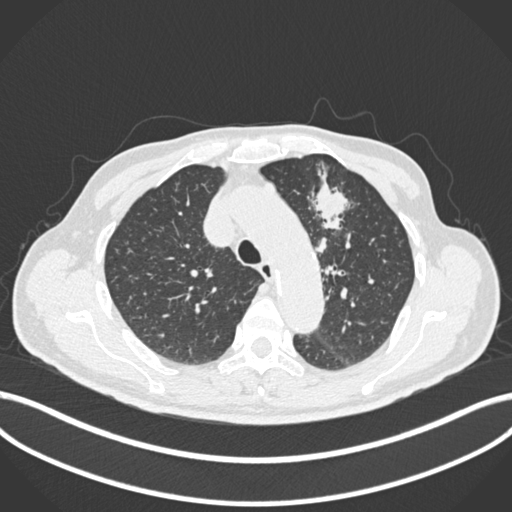
Chest CT, one axial slice. Reconstruction kernel B30f. Lung window (W 1500 / L -600 HU). 512 × 512 image matrix. Male patient, age 74 years. From the clinical record (not read from this slice): clinical TNM (as recorded): T2b N0 M1c.
Structures marked on this image (rectangle marked by the reading radiologist):
- lung tumour (recorded histology: adenocarcinoma): bounding box (x1, y1, x2, y2) in pixels: (309, 160, 351, 238)